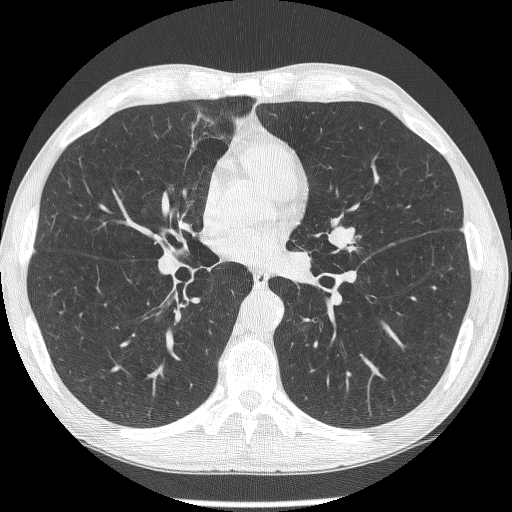
Axial slice from a low-dose chest CT screening exam, second annual screen, lung window (W 1500 / L -600 HU), 1.25 mm slice thickness, 120 kVp. Male, age 62 years at enrolment.
Expert-annotated lung lesion, bounding box [x1, y1, x2, y2] px = [320, 217, 369, 265]. The screening reader recorded 2 non-calcified nodules or masses ≥4 mm on this exam (lingula, lingula); which of them this box marks is not recorded. Official screen result: positive, other. Participant outcome: lung cancer diagnosed 95 days after this screen — small cell carcinoma, NOS, left upper lobe, stage IIIA (AJCC 6th edition).